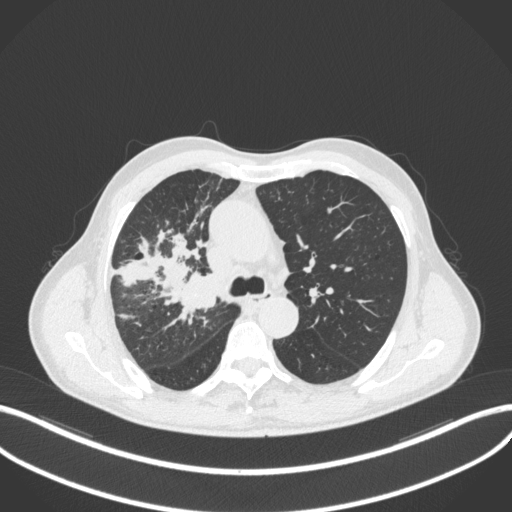
Chest CT, one axial slice; position 328 of 490 along the scan axis; lung window (W 1500 / L -600 HU); 1 mm slice thickness; 512 × 512 image matrix, field of view 400 × 400 mm. Patient: male, 69 years. From the clinical record (not read from this slice): clinical TNM (as recorded): T2a N0 M0.
Annotated regions visible in this slice (rectangle marked by the reading radiologist):
- lung tumour (recorded histology: adenocarcinoma): bounding box <178,268,224,313> (left, top, right, bottom; pixels)